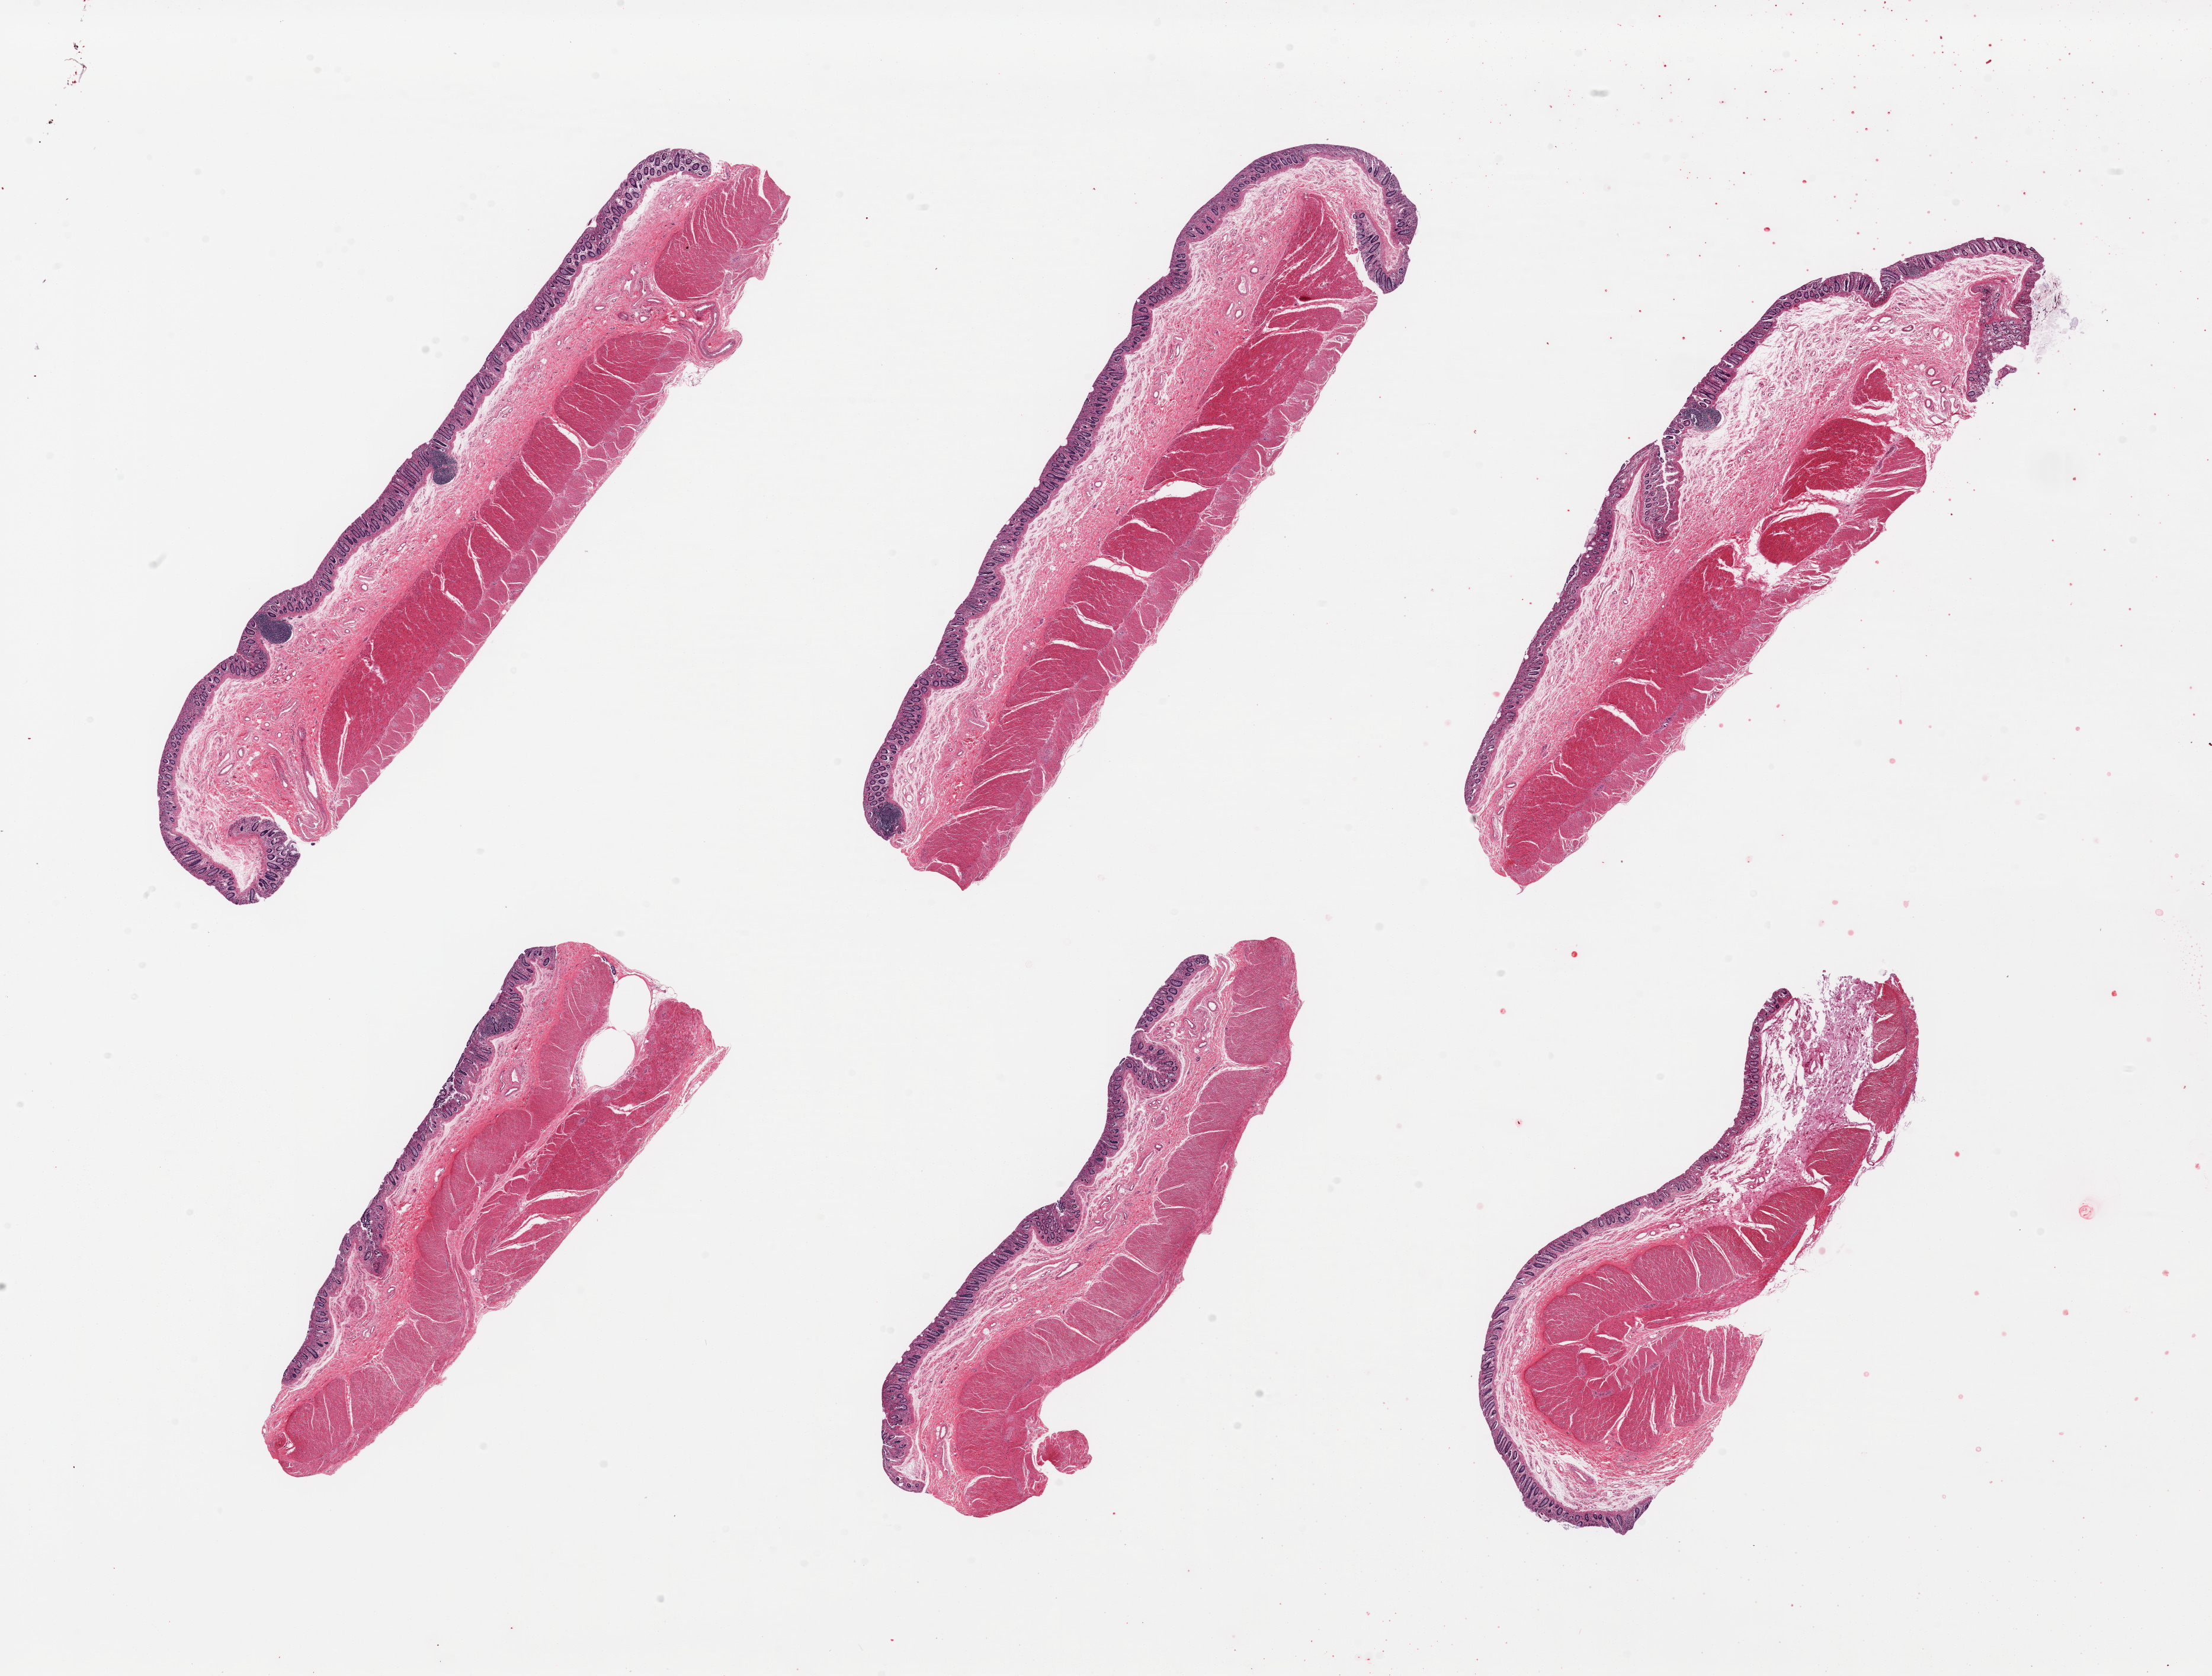
Digitized haematoxylin and eosin-stained section — a low-resolution overview of the entire scanned area, about 29.5 x 22.4 mm; PAXgene-fixed, paraffin-embedded tissue; target tissue: transverse colon; donor tissue sample. Donor: male.
* review note (as recorded): 6 pieces, mucosa up to ~0.3 mm, ~1--15% of thickness